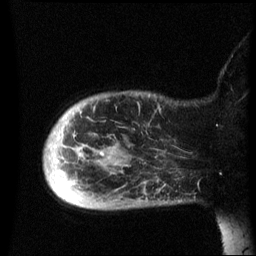
Breast MRI (dynamic contrast-enhanced), one sagittal slice. Position 9 of 60 along the scan axis. Dynamic contrast-enhanced series, image 2 of 3 at this slice position (ordered by acquisition). 1.5 T. TE 4.2 ms, TR 8.4 ms. 256 × 256 image matrix, field of view 220 × 220 mm. Patient: female, 49 years.
Annotated regions visible in this slice (semi-automatically segmented with operator editing):
- analysis volume of interest (the breast-tissue region the enhancement analysis was run in; not a lesion): bounding box (x1, y1, x2, y2) in pixels: (45, 92, 184, 211)
- tumour enhancement mask (voxels above the 70 % enhancement threshold inside the analysis volume of interest): (102, 154, 105, 157)